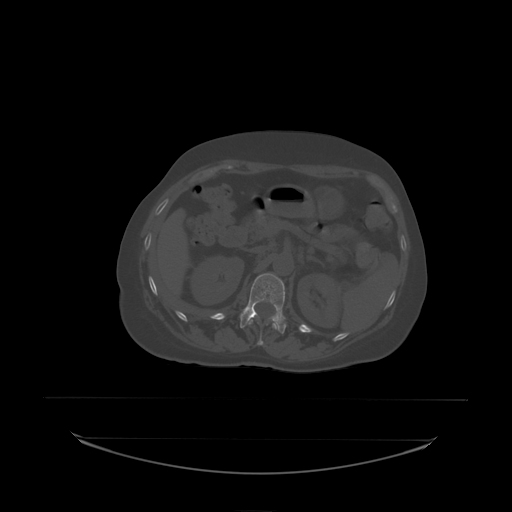
CT including the spine, one axial slice; bone window (W 1800 / L 400 HU); 2.5 mm slice thickness; 512 × 512 image matrix, field of view 500 × 500 mm. Patient: female, 53 years. Case-level facts recorded for this patient, not image findings: primary cancer: lung; vertebrae with lytic lesions (as recorded): T7, L1.
Annotated regions visible in this slice (semi-automatically segmented with operator editing):
- L1 vertebra: bounding box <240,274,287,333> (left, top, right, bottom; pixels)
- T12 vertebra: <249,320,277,330>